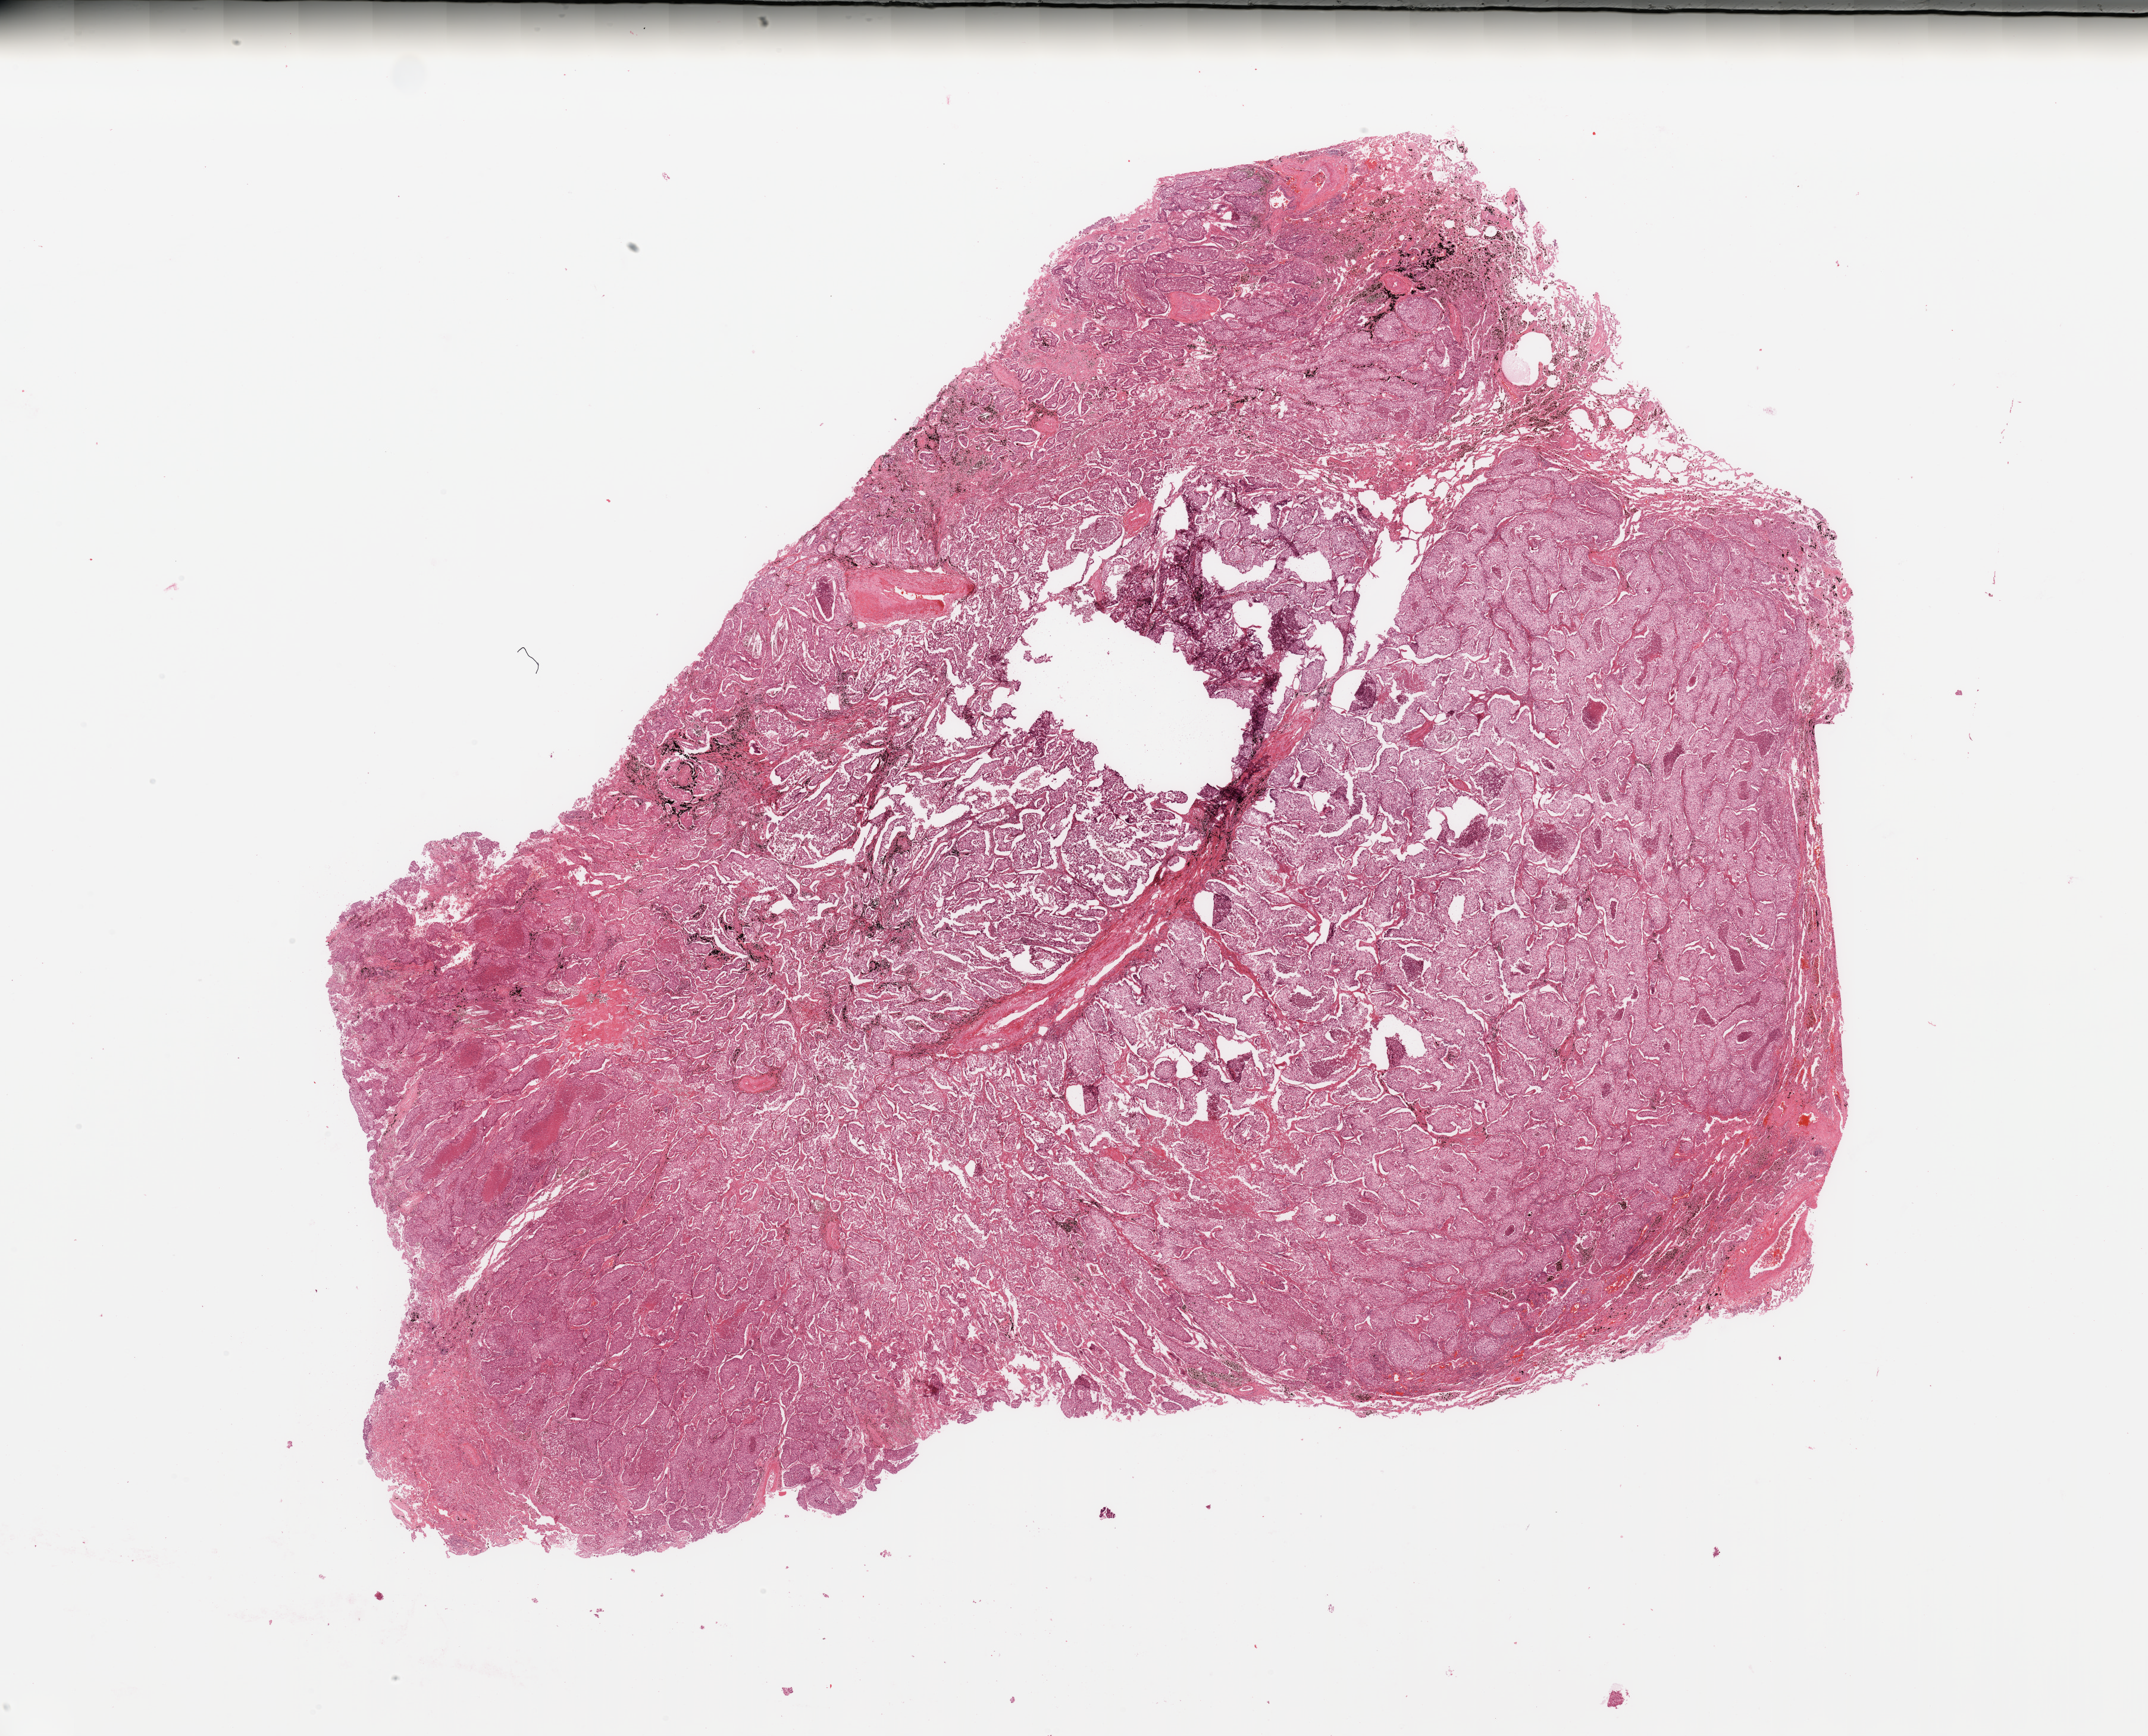
H&E whole-slide image — a low-resolution overview of the entire scanned area, about 28.5 x 23.1 mm (slide scanned at 20x). Lung, tumour tissue. 64-year-old male patient. Histologic grade: G3 (poorly differentiated).
AJCC pathologic stage: IIB. Histologic diagnosis: Adenocarcinoma, NOS.